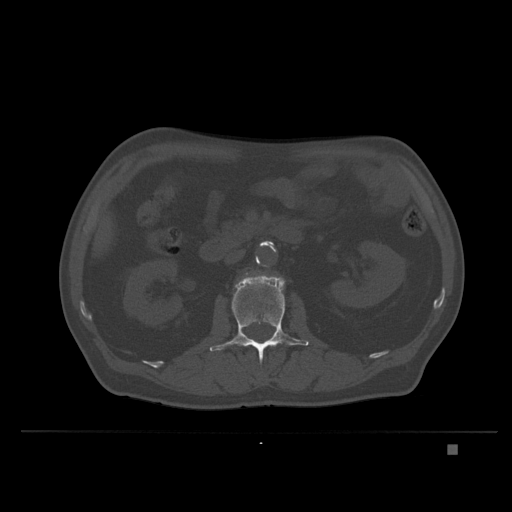
CT including the spine, one axial slice. Position 118 of 435 along the scan axis. Bone window (W 1800 / L 400 HU). 1.5 mm slice thickness. 512 × 512 image matrix, field of view 434 × 434 mm. Male patient, age 73 years. Case-level facts recorded for this patient, not image findings: primary cancer: skin.
Outlined on this slice (semi-automatic segmentation, software-assisted and operator-edited):
- L2 vertebra: bounding box <209,276,309,364> (left, top, right, bottom; pixels)